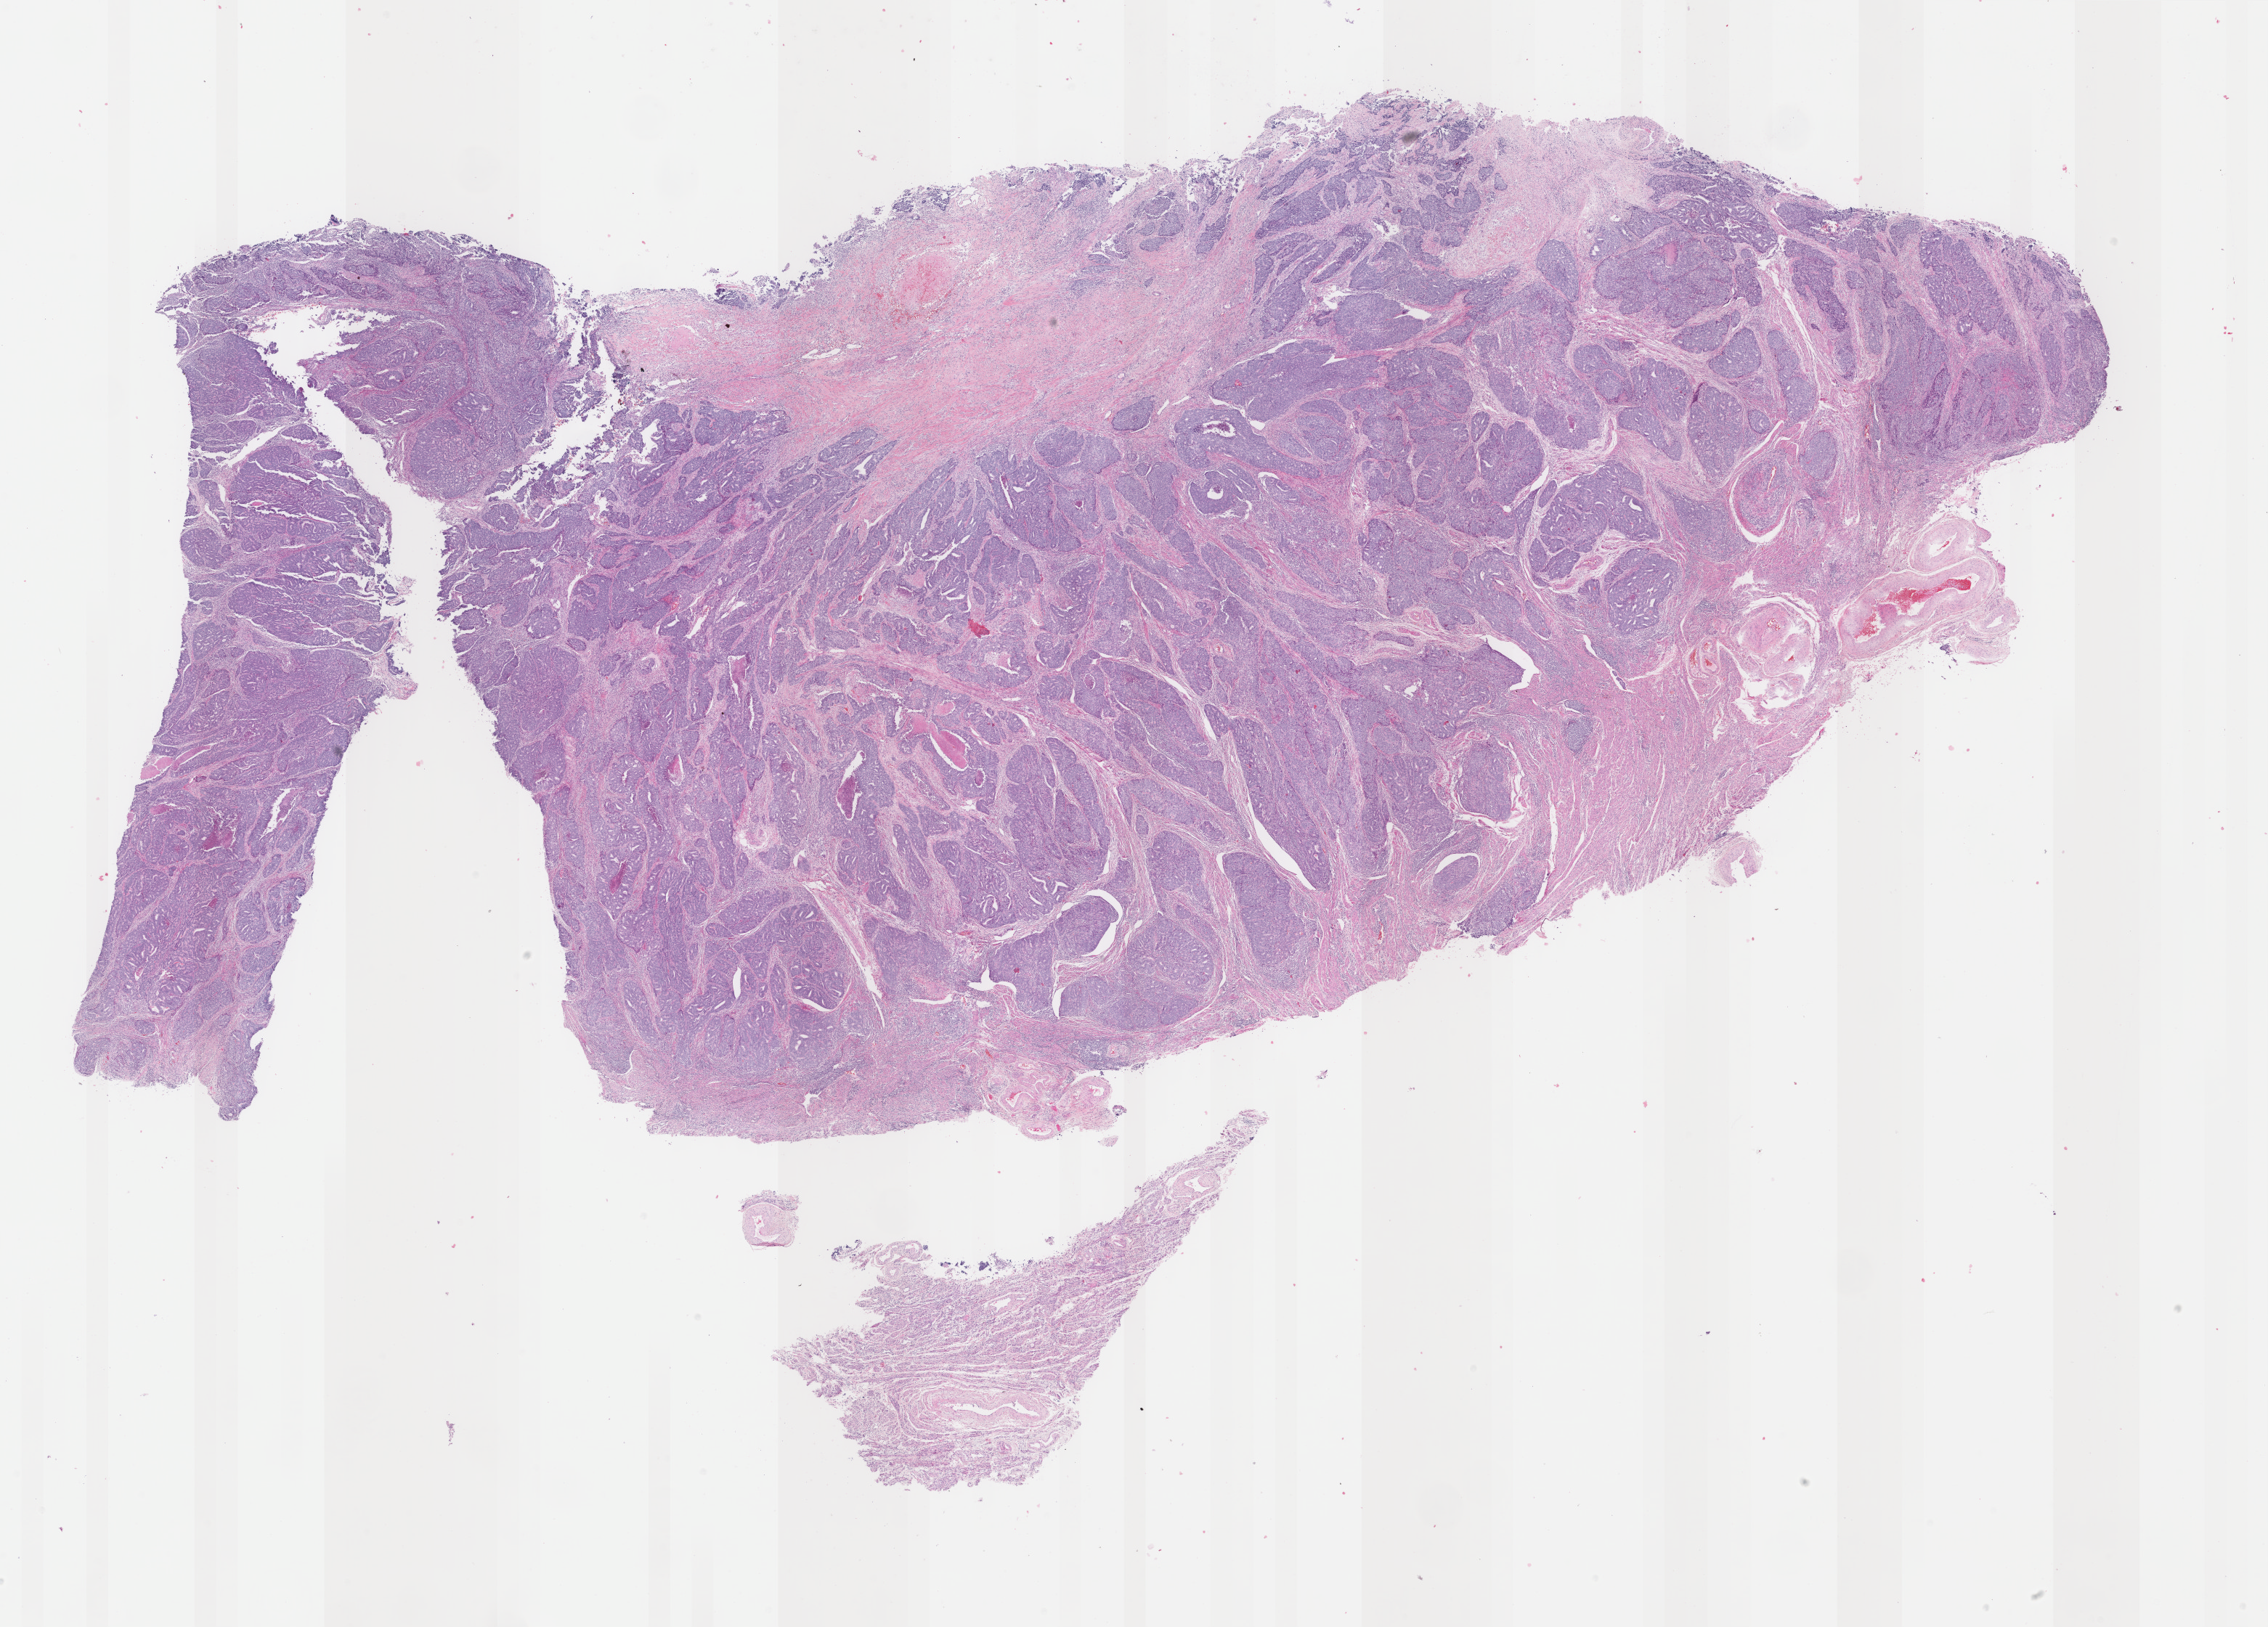
Whole-slide histology image, H&E-stained — low-resolution overview of the scanned area, about 24.8 x 17.8 mm (from a 40x scan), formalin-fixed paraffin-embedded (FFPE) diagnostic section, primary tumour sample from the uterus. Patient: female, age at initial diagnosis 73 years. Histologic grade: G3 (poorly differentiated).
* pathologic diagnosis: Endometrioid adenocarcinoma, NOS (endometrium)
* FIGO stage: IB